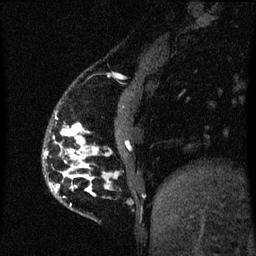
Breast MRI (dynamic contrast-enhanced), one sagittal slice. Position 12 of 60 along the scan axis. Dynamic contrast-enhanced series, image 2 of 3 at this slice position (ordered by acquisition). 1.5 T. TE 4.2 ms, TR 8 ms. 2 mm slice thickness. 256 × 256 image matrix, field of view 190 × 190 mm. Patient: female, 50 years.
Structures marked on this image (semi-automatic segmentation, software-assisted and operator-edited):
- analysis volume of interest (the breast-tissue region the enhancement analysis was run in; not a lesion): box from (x=49, y=124) to (x=96, y=191) px
- tumour enhancement mask (voxels above the 70 % enhancement threshold inside the analysis volume of interest): (x=49, y=124)–(x=91, y=191)